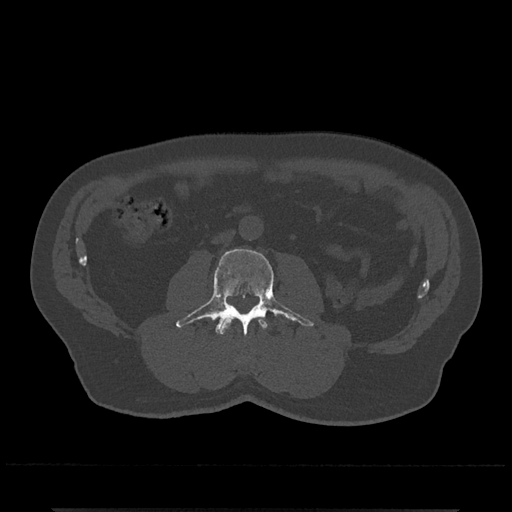
CT including the spine, one axial slice. Position 228 of 797 along the scan axis. Reconstruction kernel Br40s/3. 120 kVp. Bone window (W 1800 / L 400 HU). 512 × 512 image matrix. Patient: male, 67 years. Case-level facts recorded for this patient, not image findings: primary cancer: prostate.
Outlined on this slice (semi-automatically segmented with operator editing):
- L2 vertebra: bounding box [x1, y1, x2, y2] px = [218, 317, 267, 335]
- L3 vertebra: [175, 248, 313, 336]